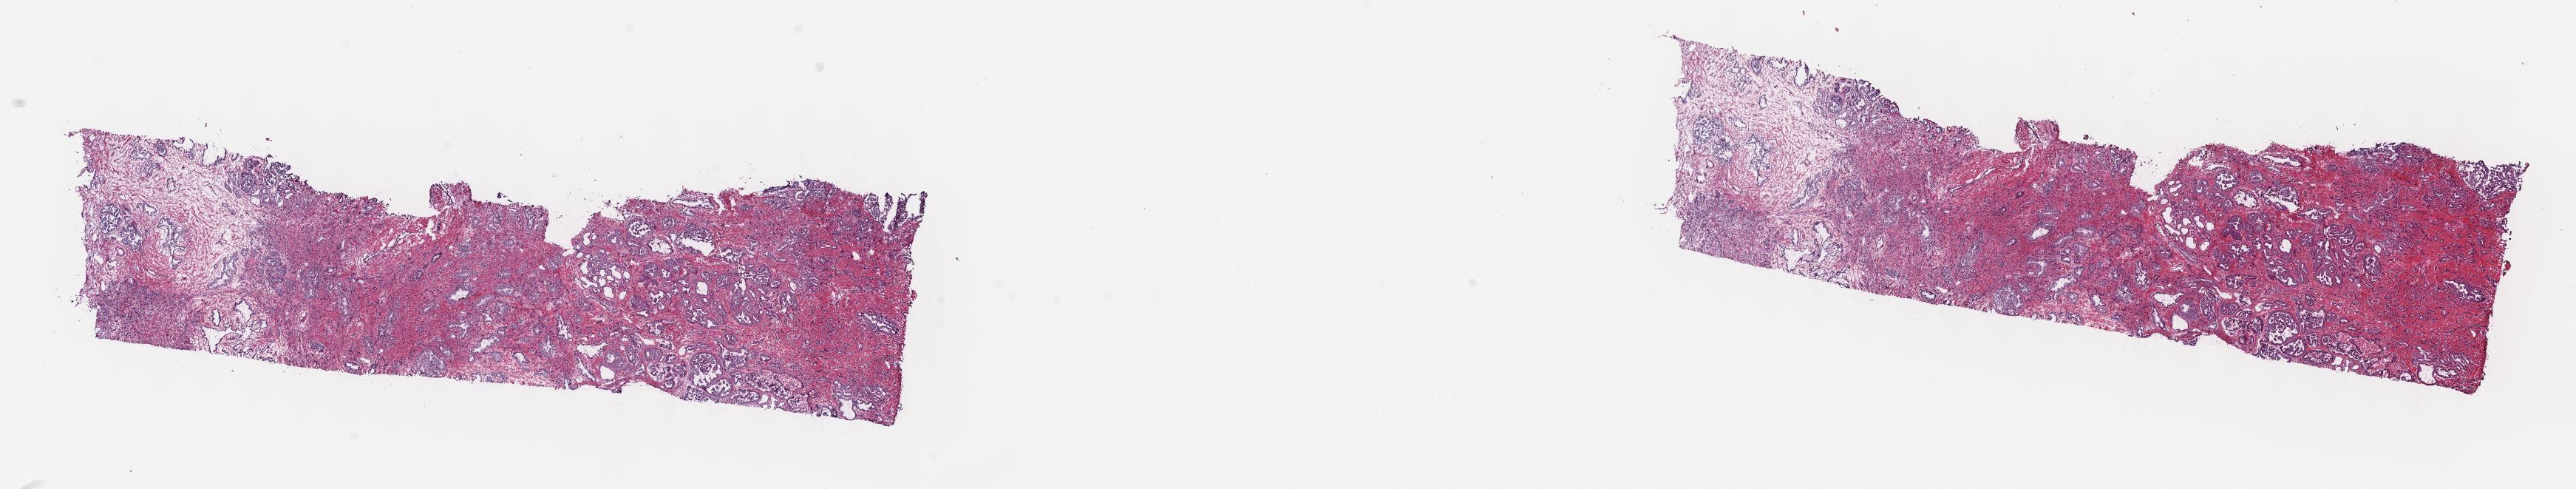
Digitized H&E tissue section (whole slide) — whole scanned area (about 28.2 x 5.3 mm) shown as a low-resolution overview, frozen section from the top of the tissue portion, prostate, primary tumour sample. Patient: male, age at initial diagnosis 60 years. Gleason score: 8 (5+3). Composition of this section per pathologist review: tumour cells 50%, tumour nuclei 60%, normal cells 30%, stromal cells 20%, necrosis 0%. Infiltration values recorded for this section: lymphocyte infiltration 0%, monocyte infiltration 0%, neutrophil infiltration 0%.
- diagnosis: Adenocarcinoma, NOS (prostate gland)
- lymph nodes positive (case pathology): 0 of 9 examined